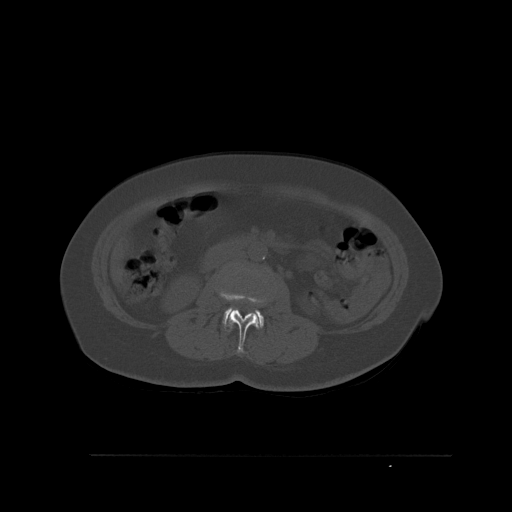
CT including the spine, one axial slice; position 239 of 527 along the scan axis; bone window (W 1800 / L 400 HU); 512 × 512 image matrix, field of view 470 × 470 mm. Female patient, age 73 years. Case-level facts recorded for this patient, not image findings: primary cancer: breast; vertebrae with lytic lesions (as recorded): L2.
Annotated regions visible in this slice (semi-automatic segmentation, software-assisted and operator-edited):
- L2 vertebra: box from (x=223, y=292) to (x=265, y=353) px
- L3 vertebra: (x=222, y=297)–(x=264, y=331)
- L4 vertebra: (x=250, y=312)–(x=261, y=329)